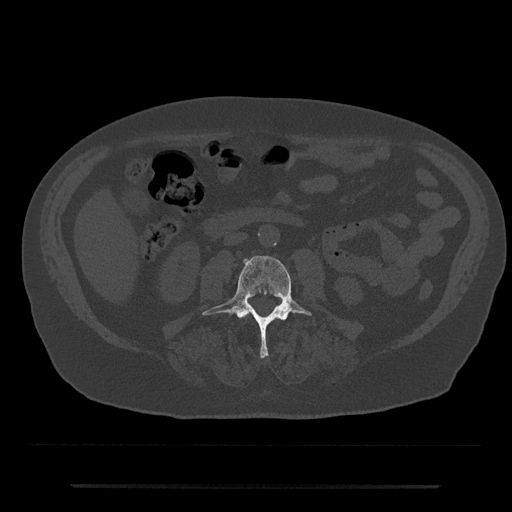
CT including the spine, one axial slice. Slice 412 of 797 in the series (ordered by position). Reconstruction kernel Br40s/3. 120 kVp. Bone window (W 1800 / L 400 HU). 0.5 mm slice thickness. 512 × 512 image matrix. Patient: male, 80 years. Case-level facts recorded for this patient, not image findings: primary cancer: prostate; vertebrae with lytic lesions (as recorded): L1, T11.
Structures marked on this image (semi-automatically segmented with operator editing):
- L3 vertebra: bounding box [x1, y1, x2, y2] px = [203, 256, 312, 359]